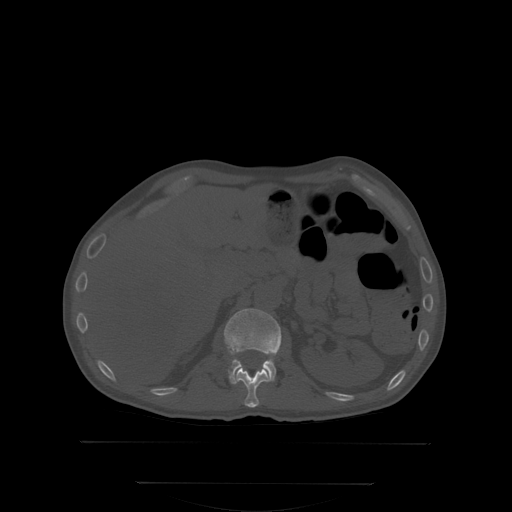
CT including the spine, one axial slice. Position 160 of 350 along the scan axis. Bone window (W 1800 / L 400 HU). 2.5 mm slice thickness. 512 × 512 image matrix, field of view 500 × 500 mm. Patient: male, 58 years. From the clinical record (not read from this slice): primary cancer: prostate; vertebrae with lytic lesions (as recorded): L1.
Structures marked on this image (semi-automatically segmented with operator editing):
- L1 vertebra: bounding box (x1, y1, x2, y2) in pixels: (225, 308, 280, 383)
- T12 vertebra: (236, 366, 270, 408)